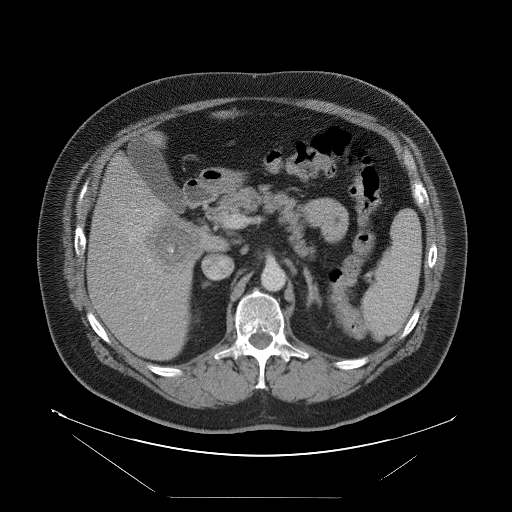
Contrast-enhanced abdominal CT, one axial slice. Position 50 of 114 along the scan axis. Soft-tissue window (W 400 / L 40 HU). 512 × 512 image matrix, field of view 500 × 500 mm. Male patient, age 61 years. Case-level facts recorded for this patient, not image findings: diagnosis: colorectal cancer liver metastases, imaged before liver resection; multiple liver metastases: no; largest metastasis: 6.5 cm; disease in both lobes: yes.
Outlined on this slice (manually delineated by an expert):
- liver: bounding box [x1, y1, x2, y2] px = [89, 137, 224, 360]
- liver metastasis: [149, 217, 201, 266]